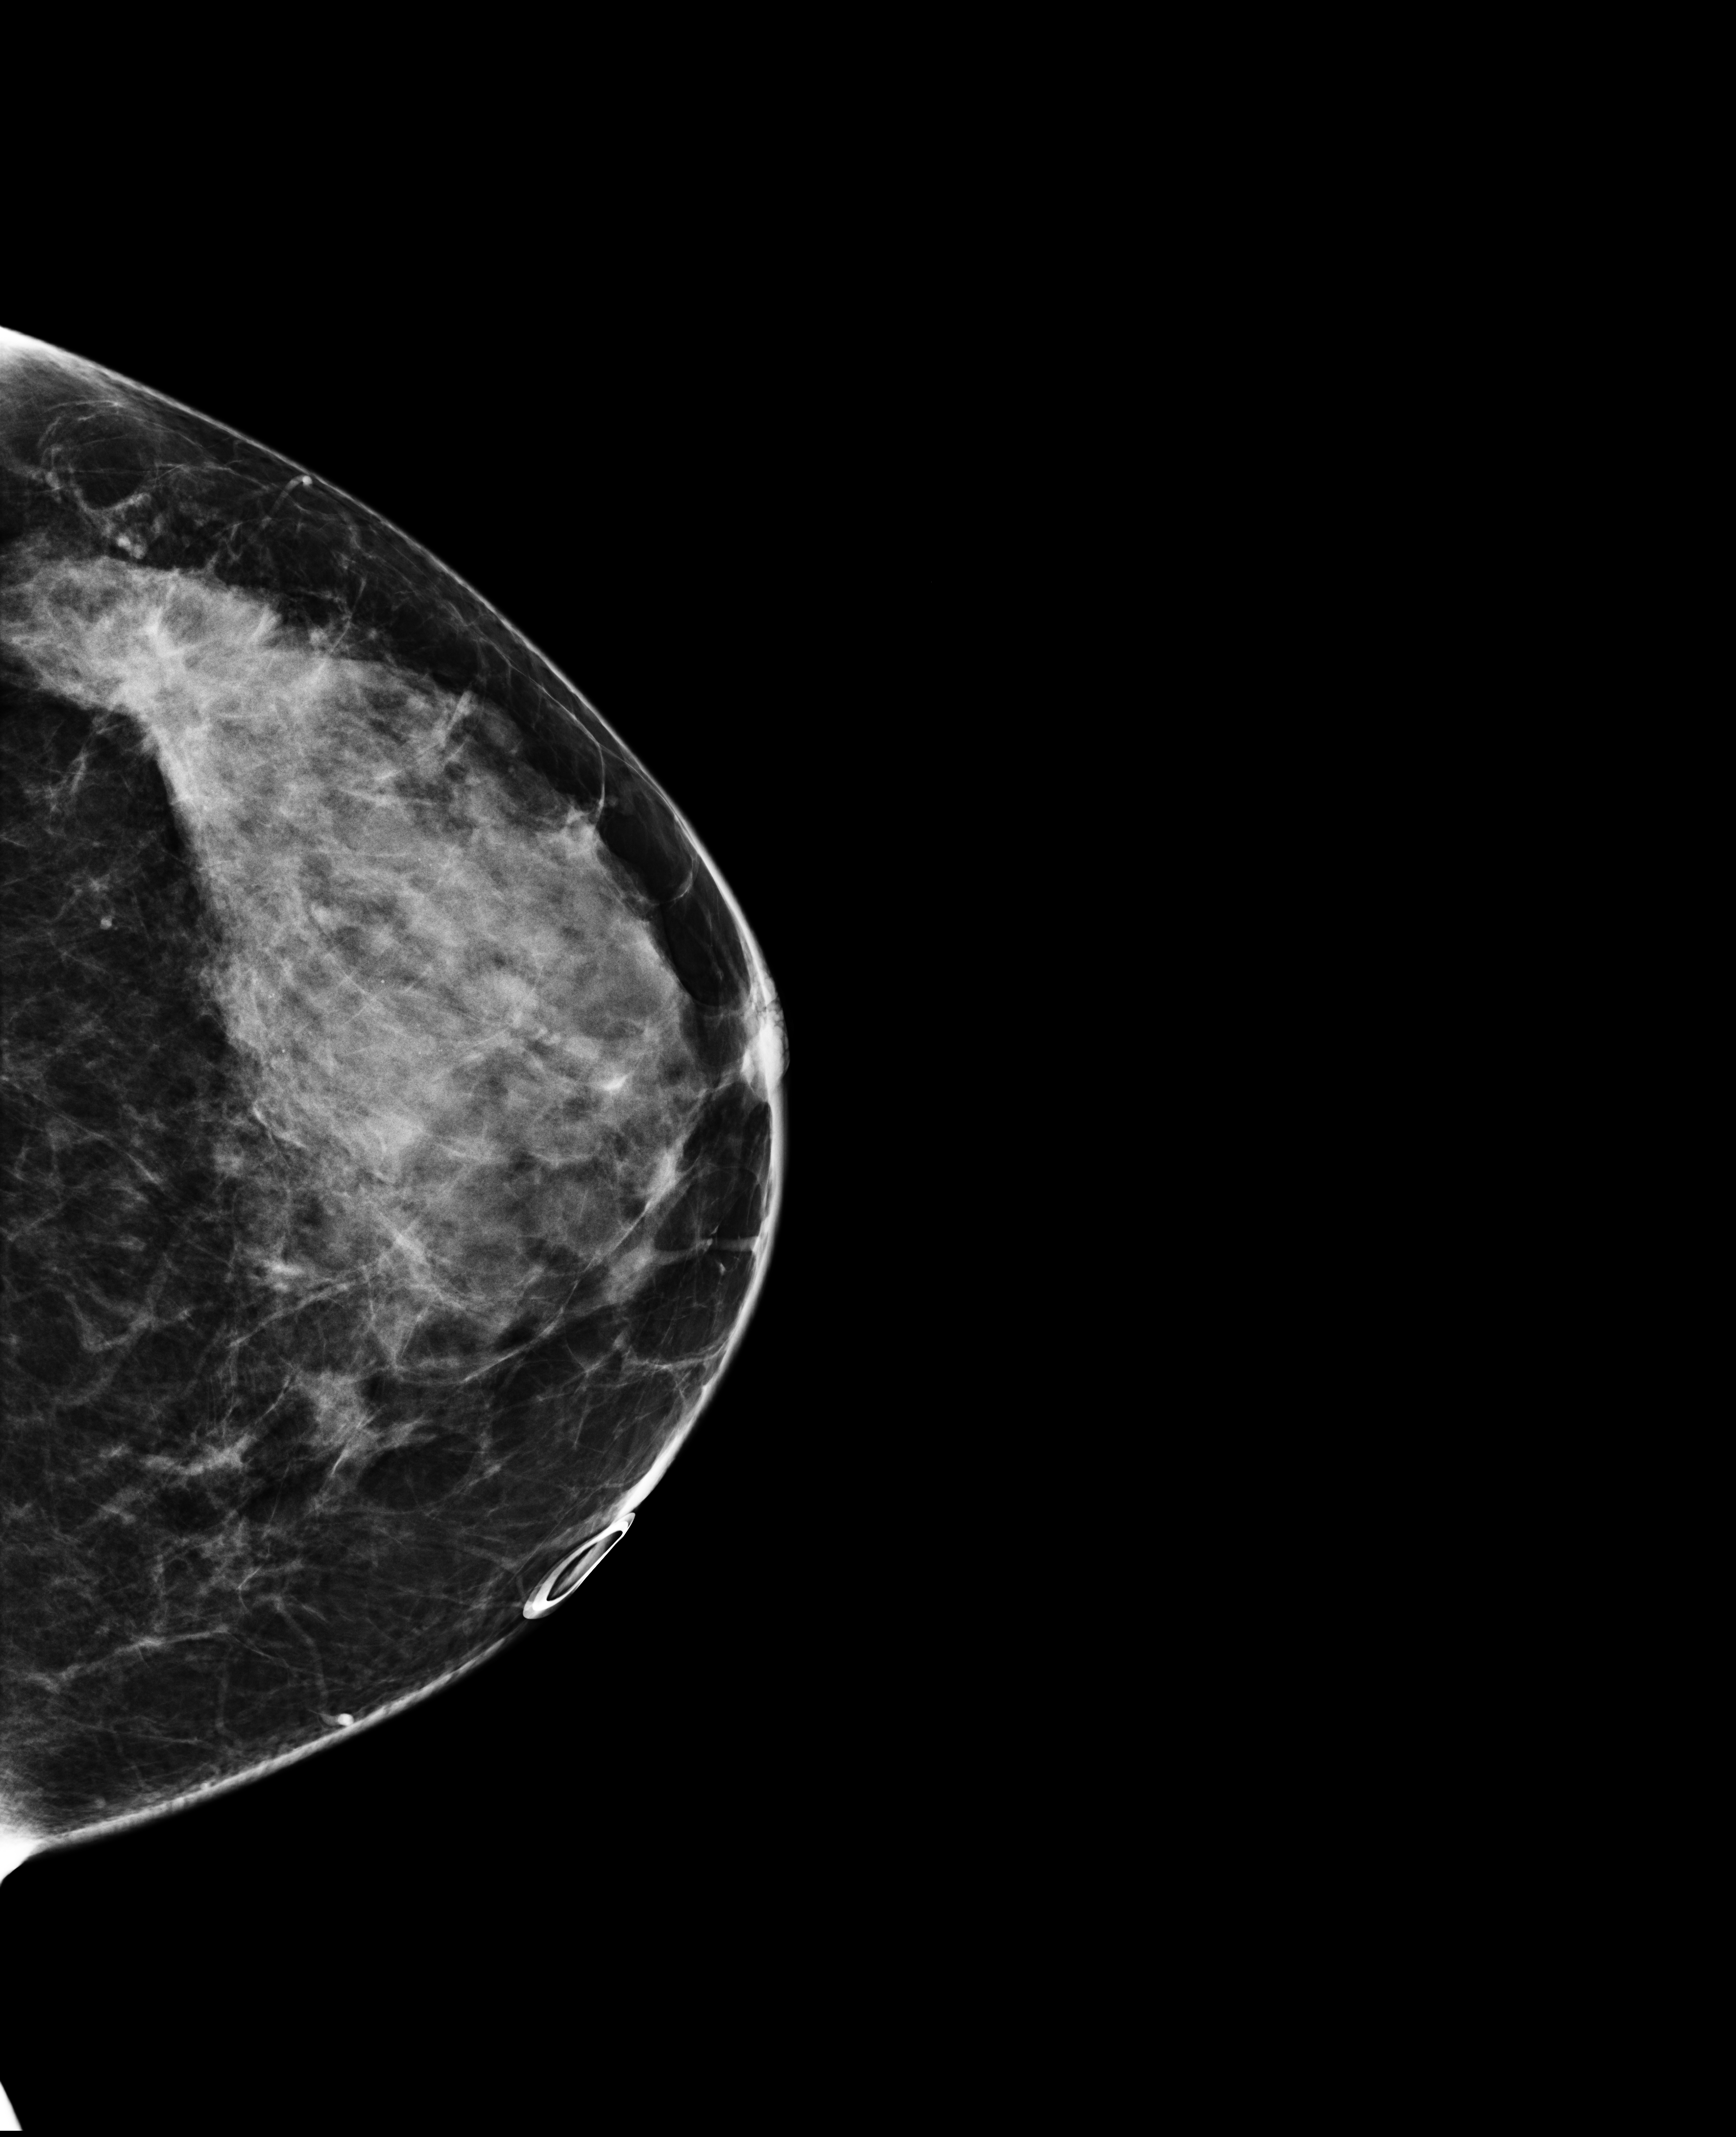
Full-field digital mammogram (FFDM), left breast, CC view, annual screening mammography examination, compressed breast thickness 57 mm. Female patient, age 46 years.
Breast density at the screening exam (both breasts): heterogeneously dense (BI-RADS density category c). Final BI-RADS assessment for this screening round (tomosynthesis exam, both breasts): category 5. Recall: no recall after this screen.